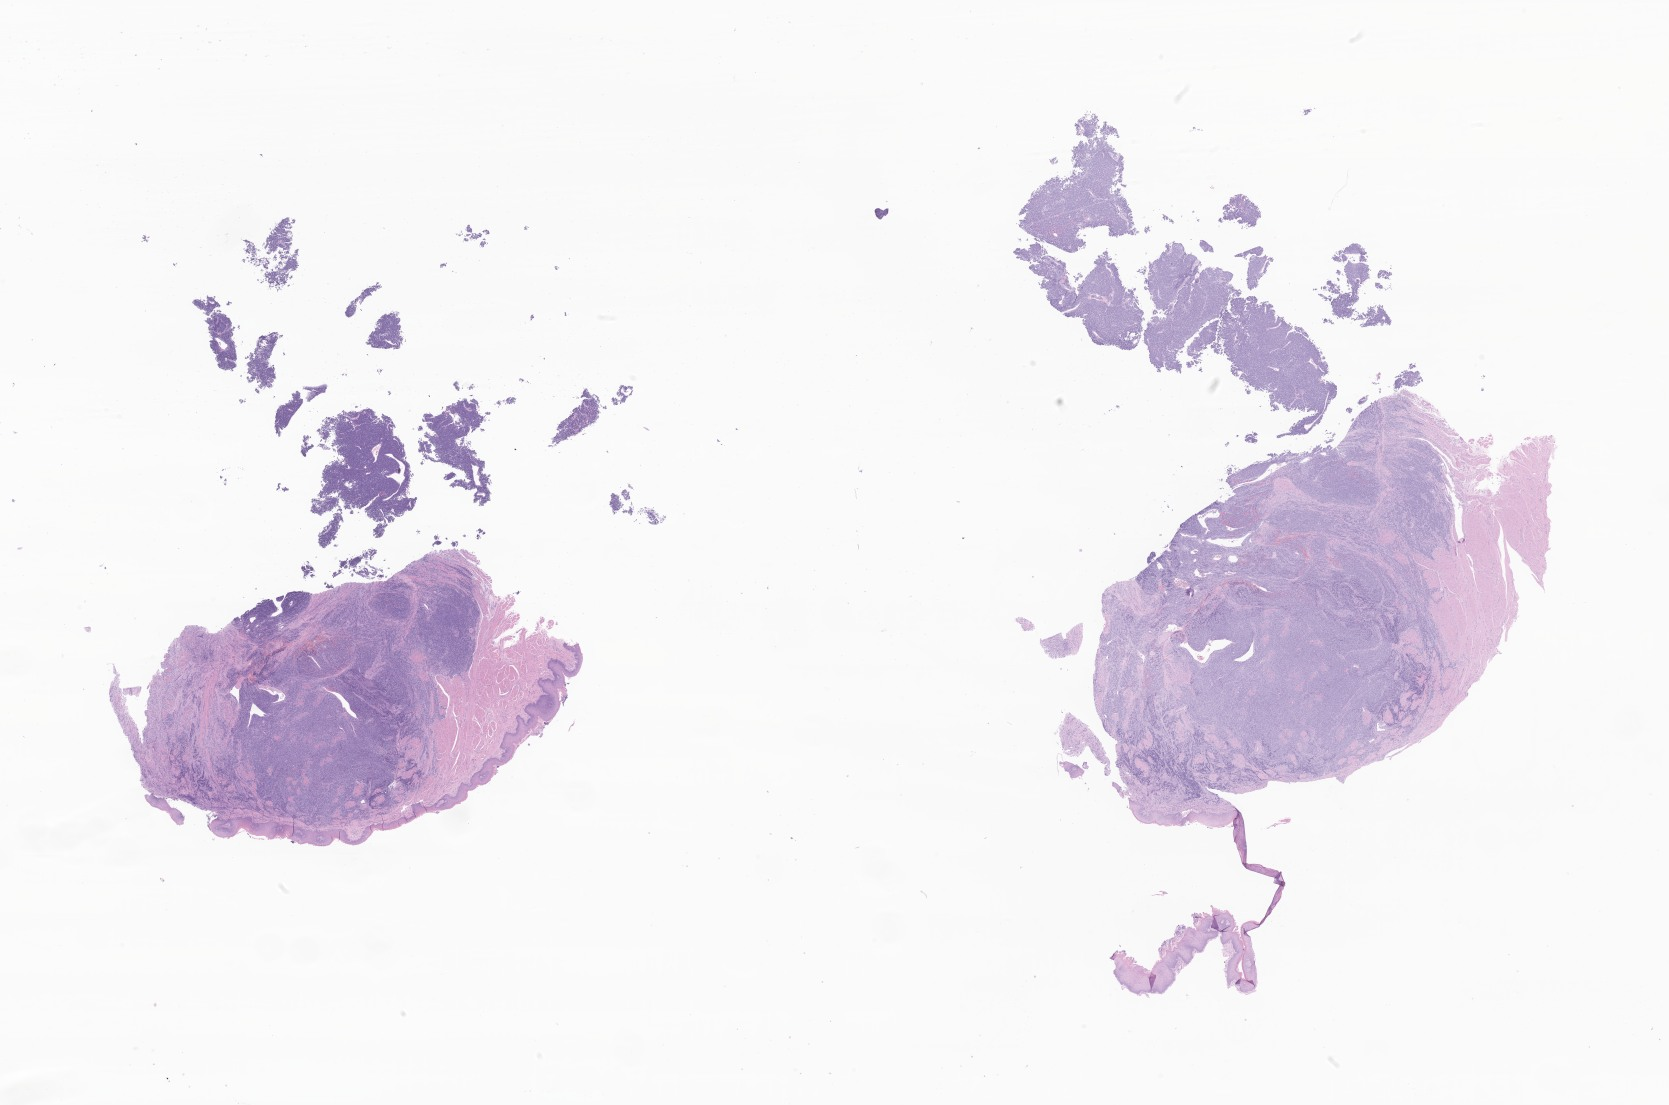
Digitized hematoxylin and eosin (H&E)-stained section of tumor tissue from the tongue — low-resolution overview of the scanned area, about 28.1 x 18.6 mm; formalin-fixed paraffin-embedded section. Female patient, age 763 days (about 2.1 years).
Recorded diagnosis: Rhabdomyosarcoma, NOS.